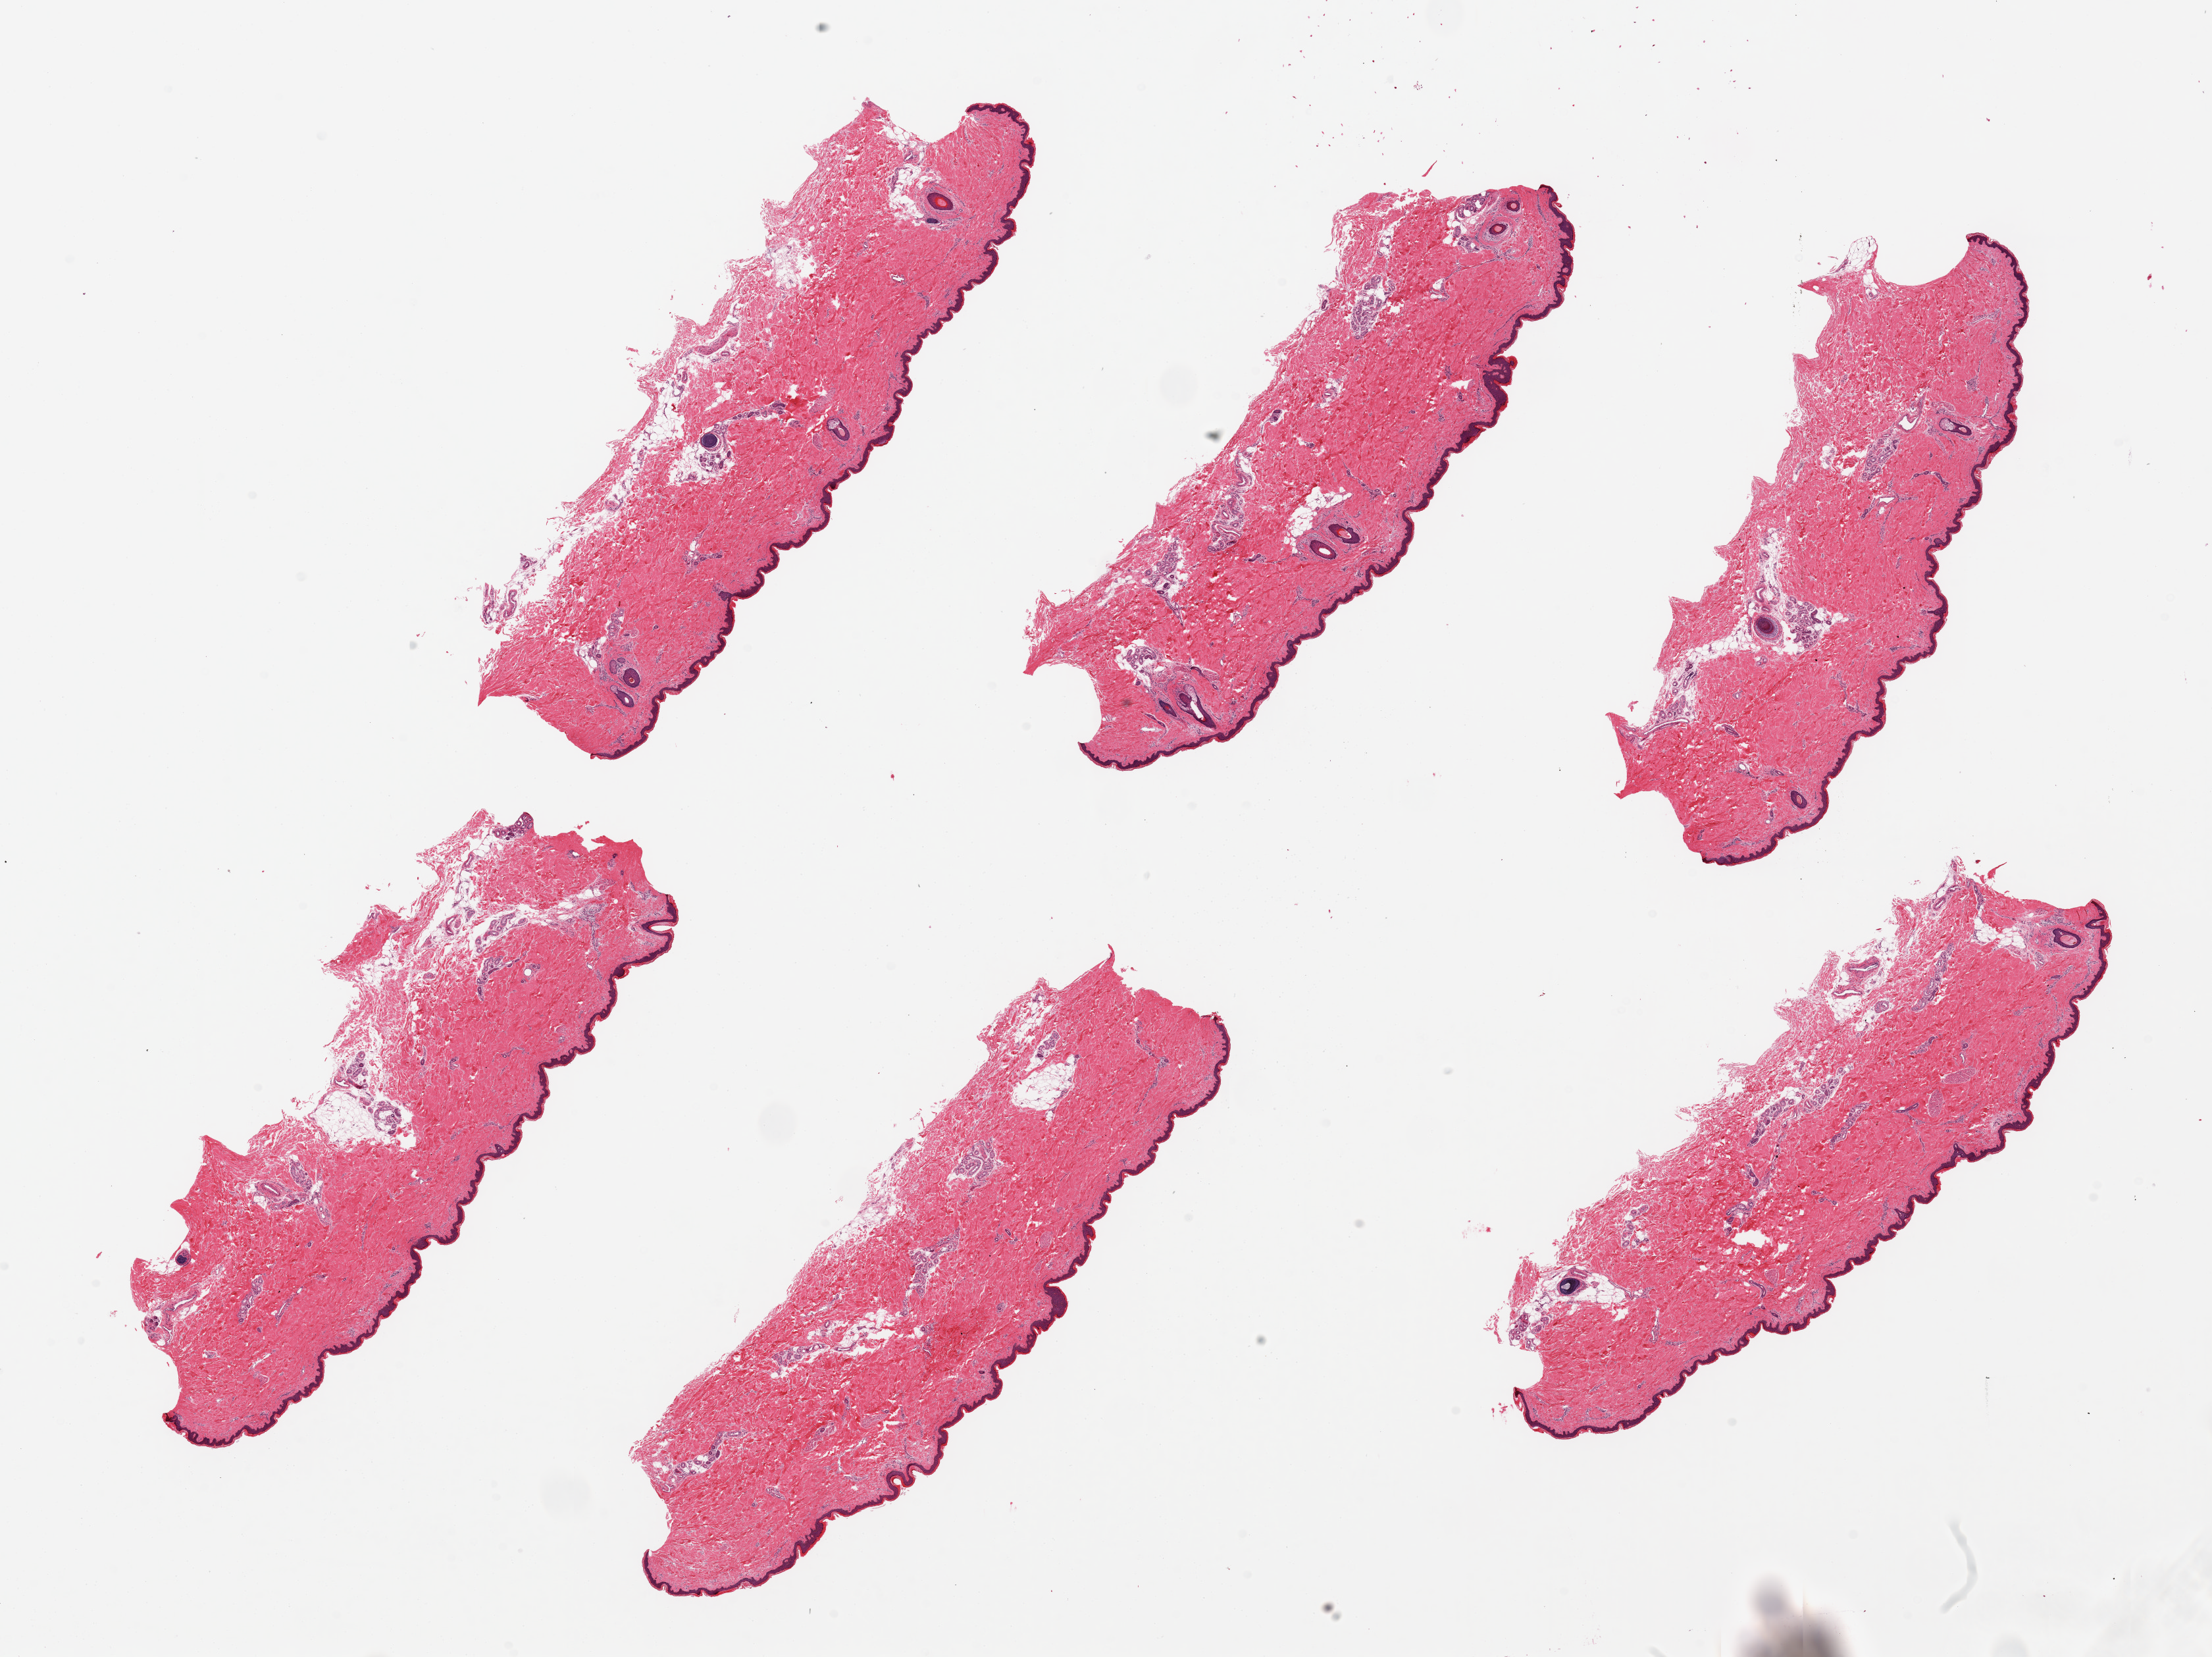
Whole-slide image, hematoxylin and eosin (H&E) stain, shown as a low-resolution overview of the whole scanned area (about 26.6 x 19.9 mm, acquisition: 20x scan); PAXgene-fixed, paraffin-embedded tissue; sampled site (target tissue): skin of lower leg; tissue donor sample. Donor: male.
Pathologist's review note for this sample: 6 pieces, up to 9.5x3mm; well trimmed subcutaneous adipose tissue.